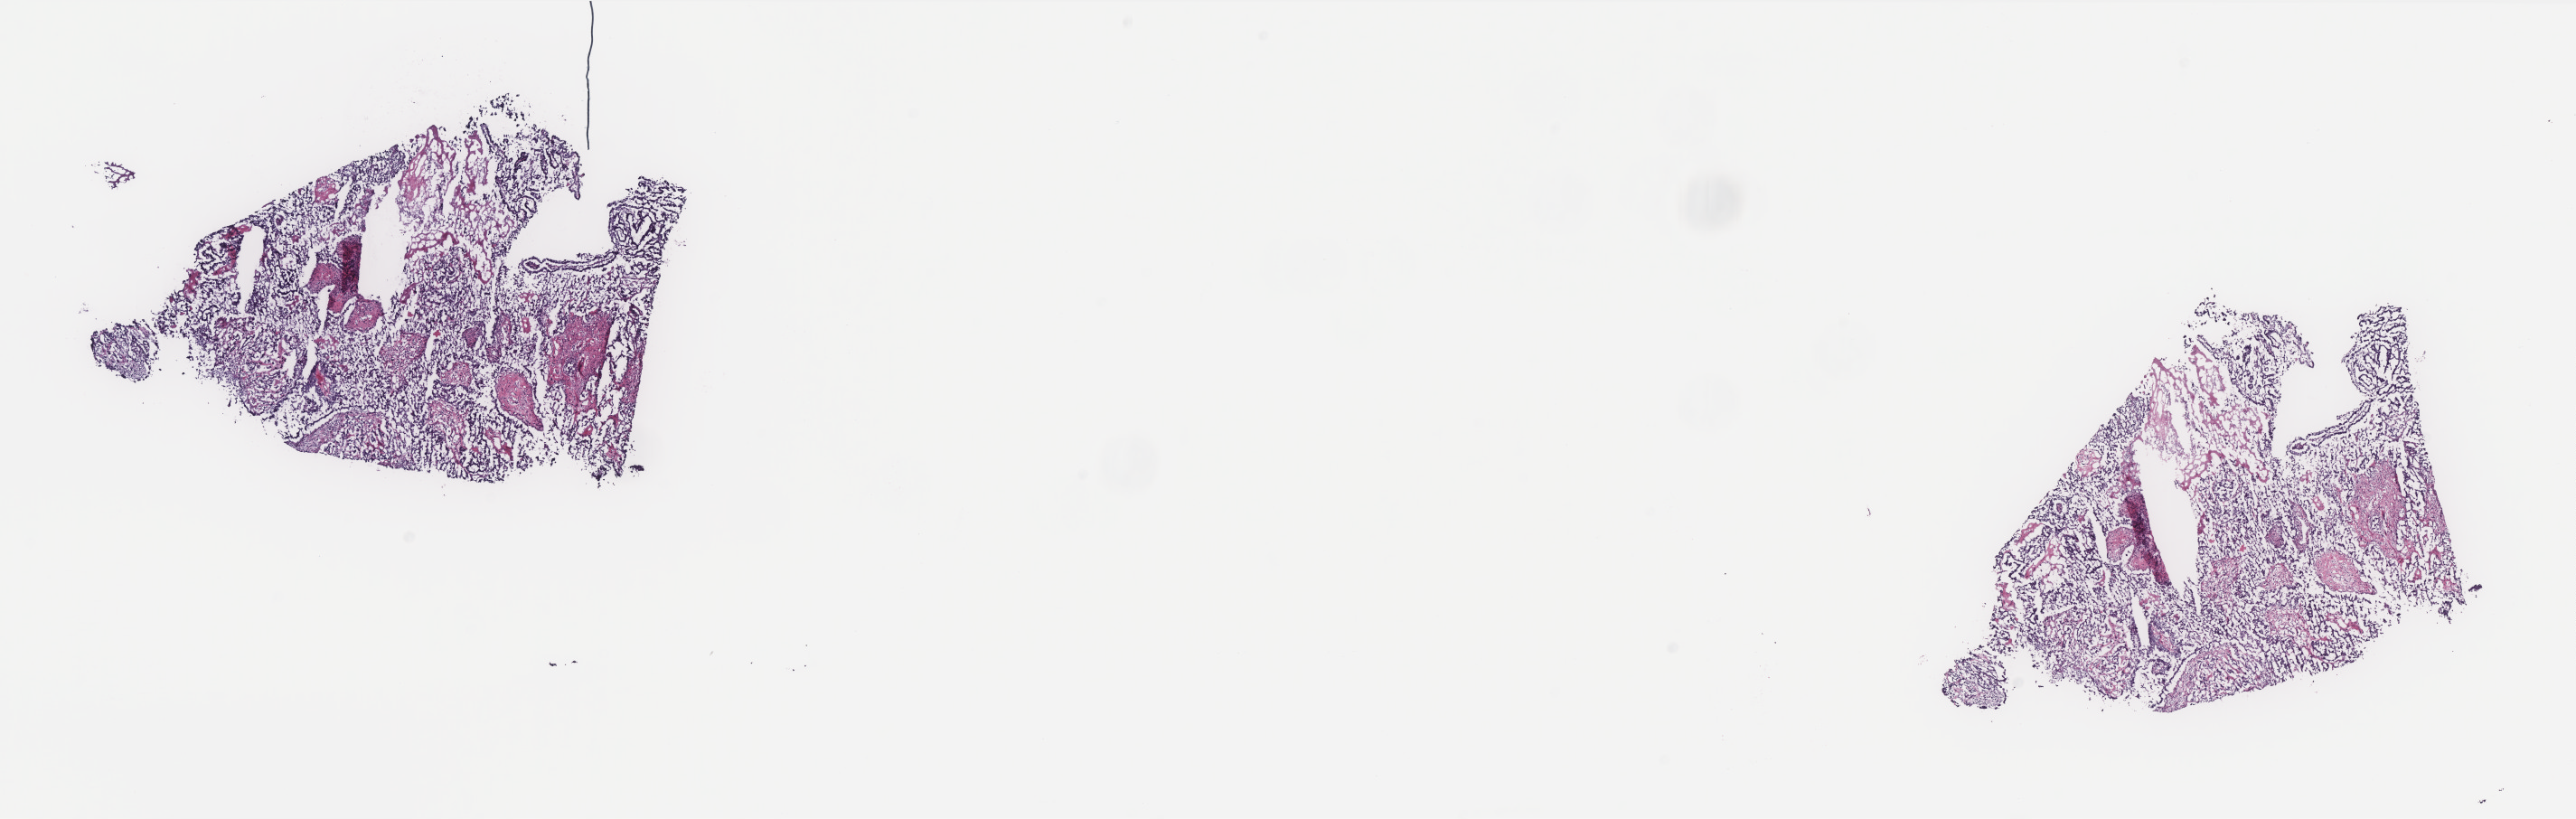
Digitized H&E tissue section (whole slide), a low-resolution overview of the entire scanned area, about 22.8 x 7.3 mm, frozen section from the top of the tissue portion, primary tumour sample from the uterus. Female patient; age at initial diagnosis 62 years. Histologic grade: G3 (poorly differentiated). Slide review estimates, as recorded: tumour cells 75%, tumour nuclei 80%, normal cells 0%, stromal cells 20%, necrosis 5%. Inflammatory infiltration, as recorded: lymphocyte infiltration 3%, monocyte infiltration 3%, neutrophil infiltration 0%.
FIGO stage: IIIC2. Pathologic diagnosis: Serous cystadenocarcinoma, NOS (endometrium).